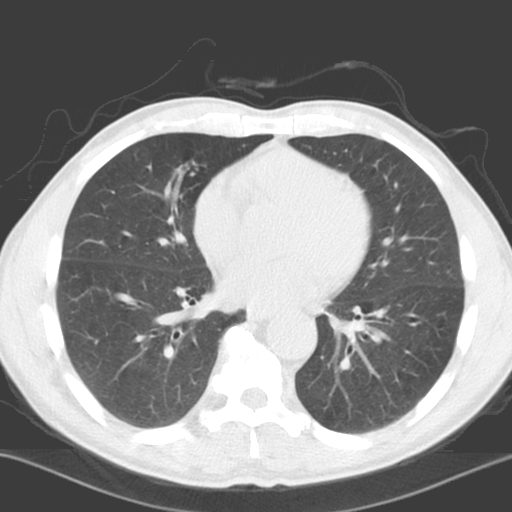
Low-dose screening chest CT, axial slice; baseline screening round; lung window (W 1500 / L -600 HU). Male, age 65 years at enrolment. Current smoker at enrolment.
Lesion marked by an expert reader, bounding box <144,155,204,219> (left, top, right, bottom; pixels). Screening reader's record for this exam (one nodule recorded; not confirmed to be the boxed lesion): non-calcified nodule or mass ≥4 mm, right lower lobe, 5 × 5 mm, poorly defined margins, soft tissue attenuation. Lung cancer was diagnosed 1144 days after this screen (after the third annual screen): squamous cell carcinoma, NOS, right middle lobe, poorly differentiated (G3), stage IA (AJCC 6th edition), 23 mm at pathology.